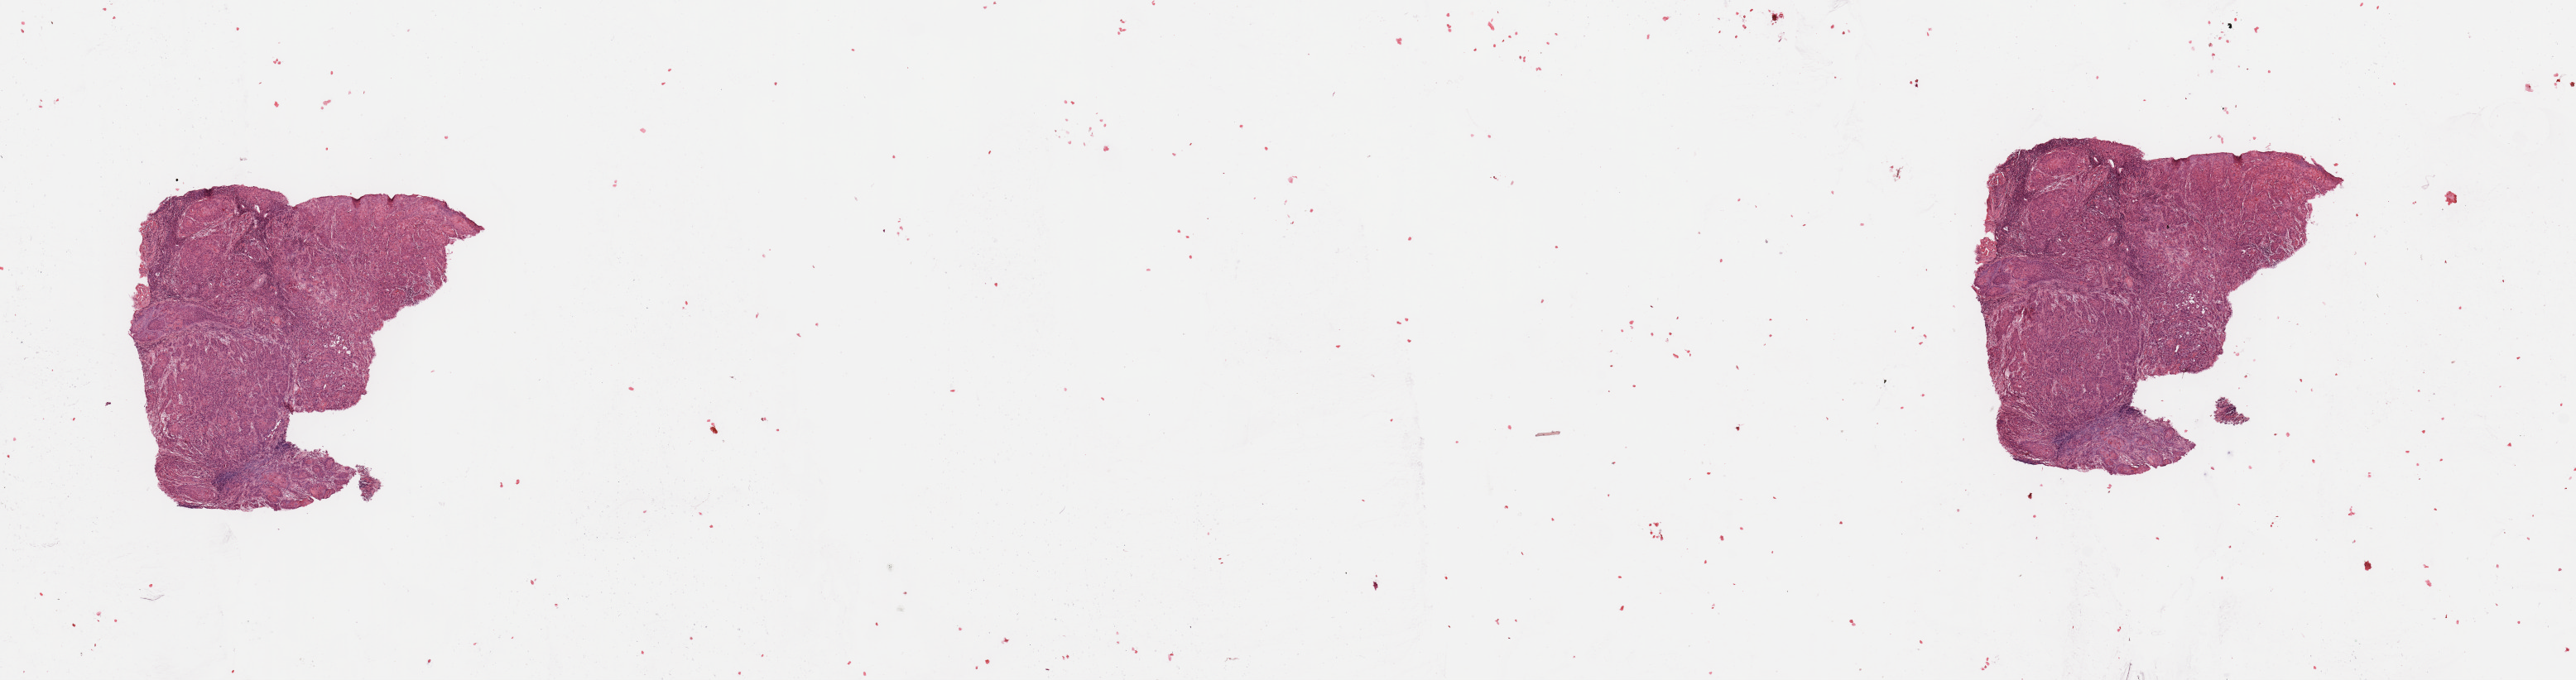
Whole-slide histology image, H&E-stained, whole scanned area (about 24.6 x 6.5 mm) shown as a low-resolution overview, tumour tissue sample, sampled site: tongue. 53-year-old male patient. Histologic grade: G2 (moderately differentiated). Composition of this section per pathologist review: tumour nuclei 90%, necrosis 5%.
- primary tumour site (as recorded): oral cavity
- AJCC pathologic stage: II
- diagnosis: Squamous cell carcinoma, NOS (tongue, NOS)